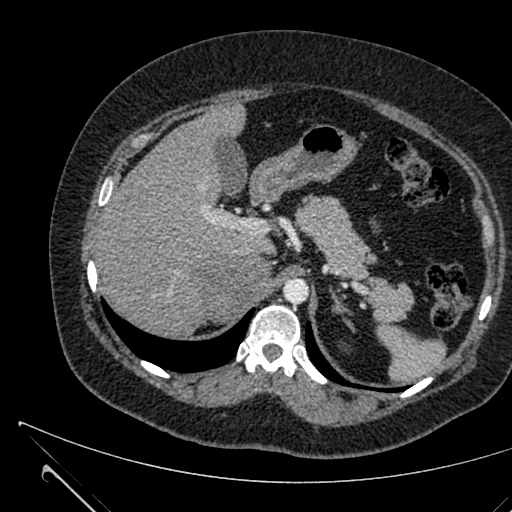
Contrast-enhanced abdominal CT, one axial slice. Slice 463 of 731 in the series (ordered by position). 120 kVp. Intravenous contrast given. Soft-tissue window (W 400 / L 40 HU). 1 mm slice thickness. 512 × 512 image matrix, field of view 376 × 376 mm. Female patient, age 36 years. Case-level facts recorded for this patient, not image findings: diagnosis: adrenocortical carcinoma; tumour side: right adrenal; tumour size at pathology: 10 cm; Ki-67 index: 20 %; stage (as recorded): 4.
Annotated regions visible in this slice (semi-automatic segmentation, software-assisted and operator-edited):
- mass: box from (x=202, y=257) to (x=268, y=322) px